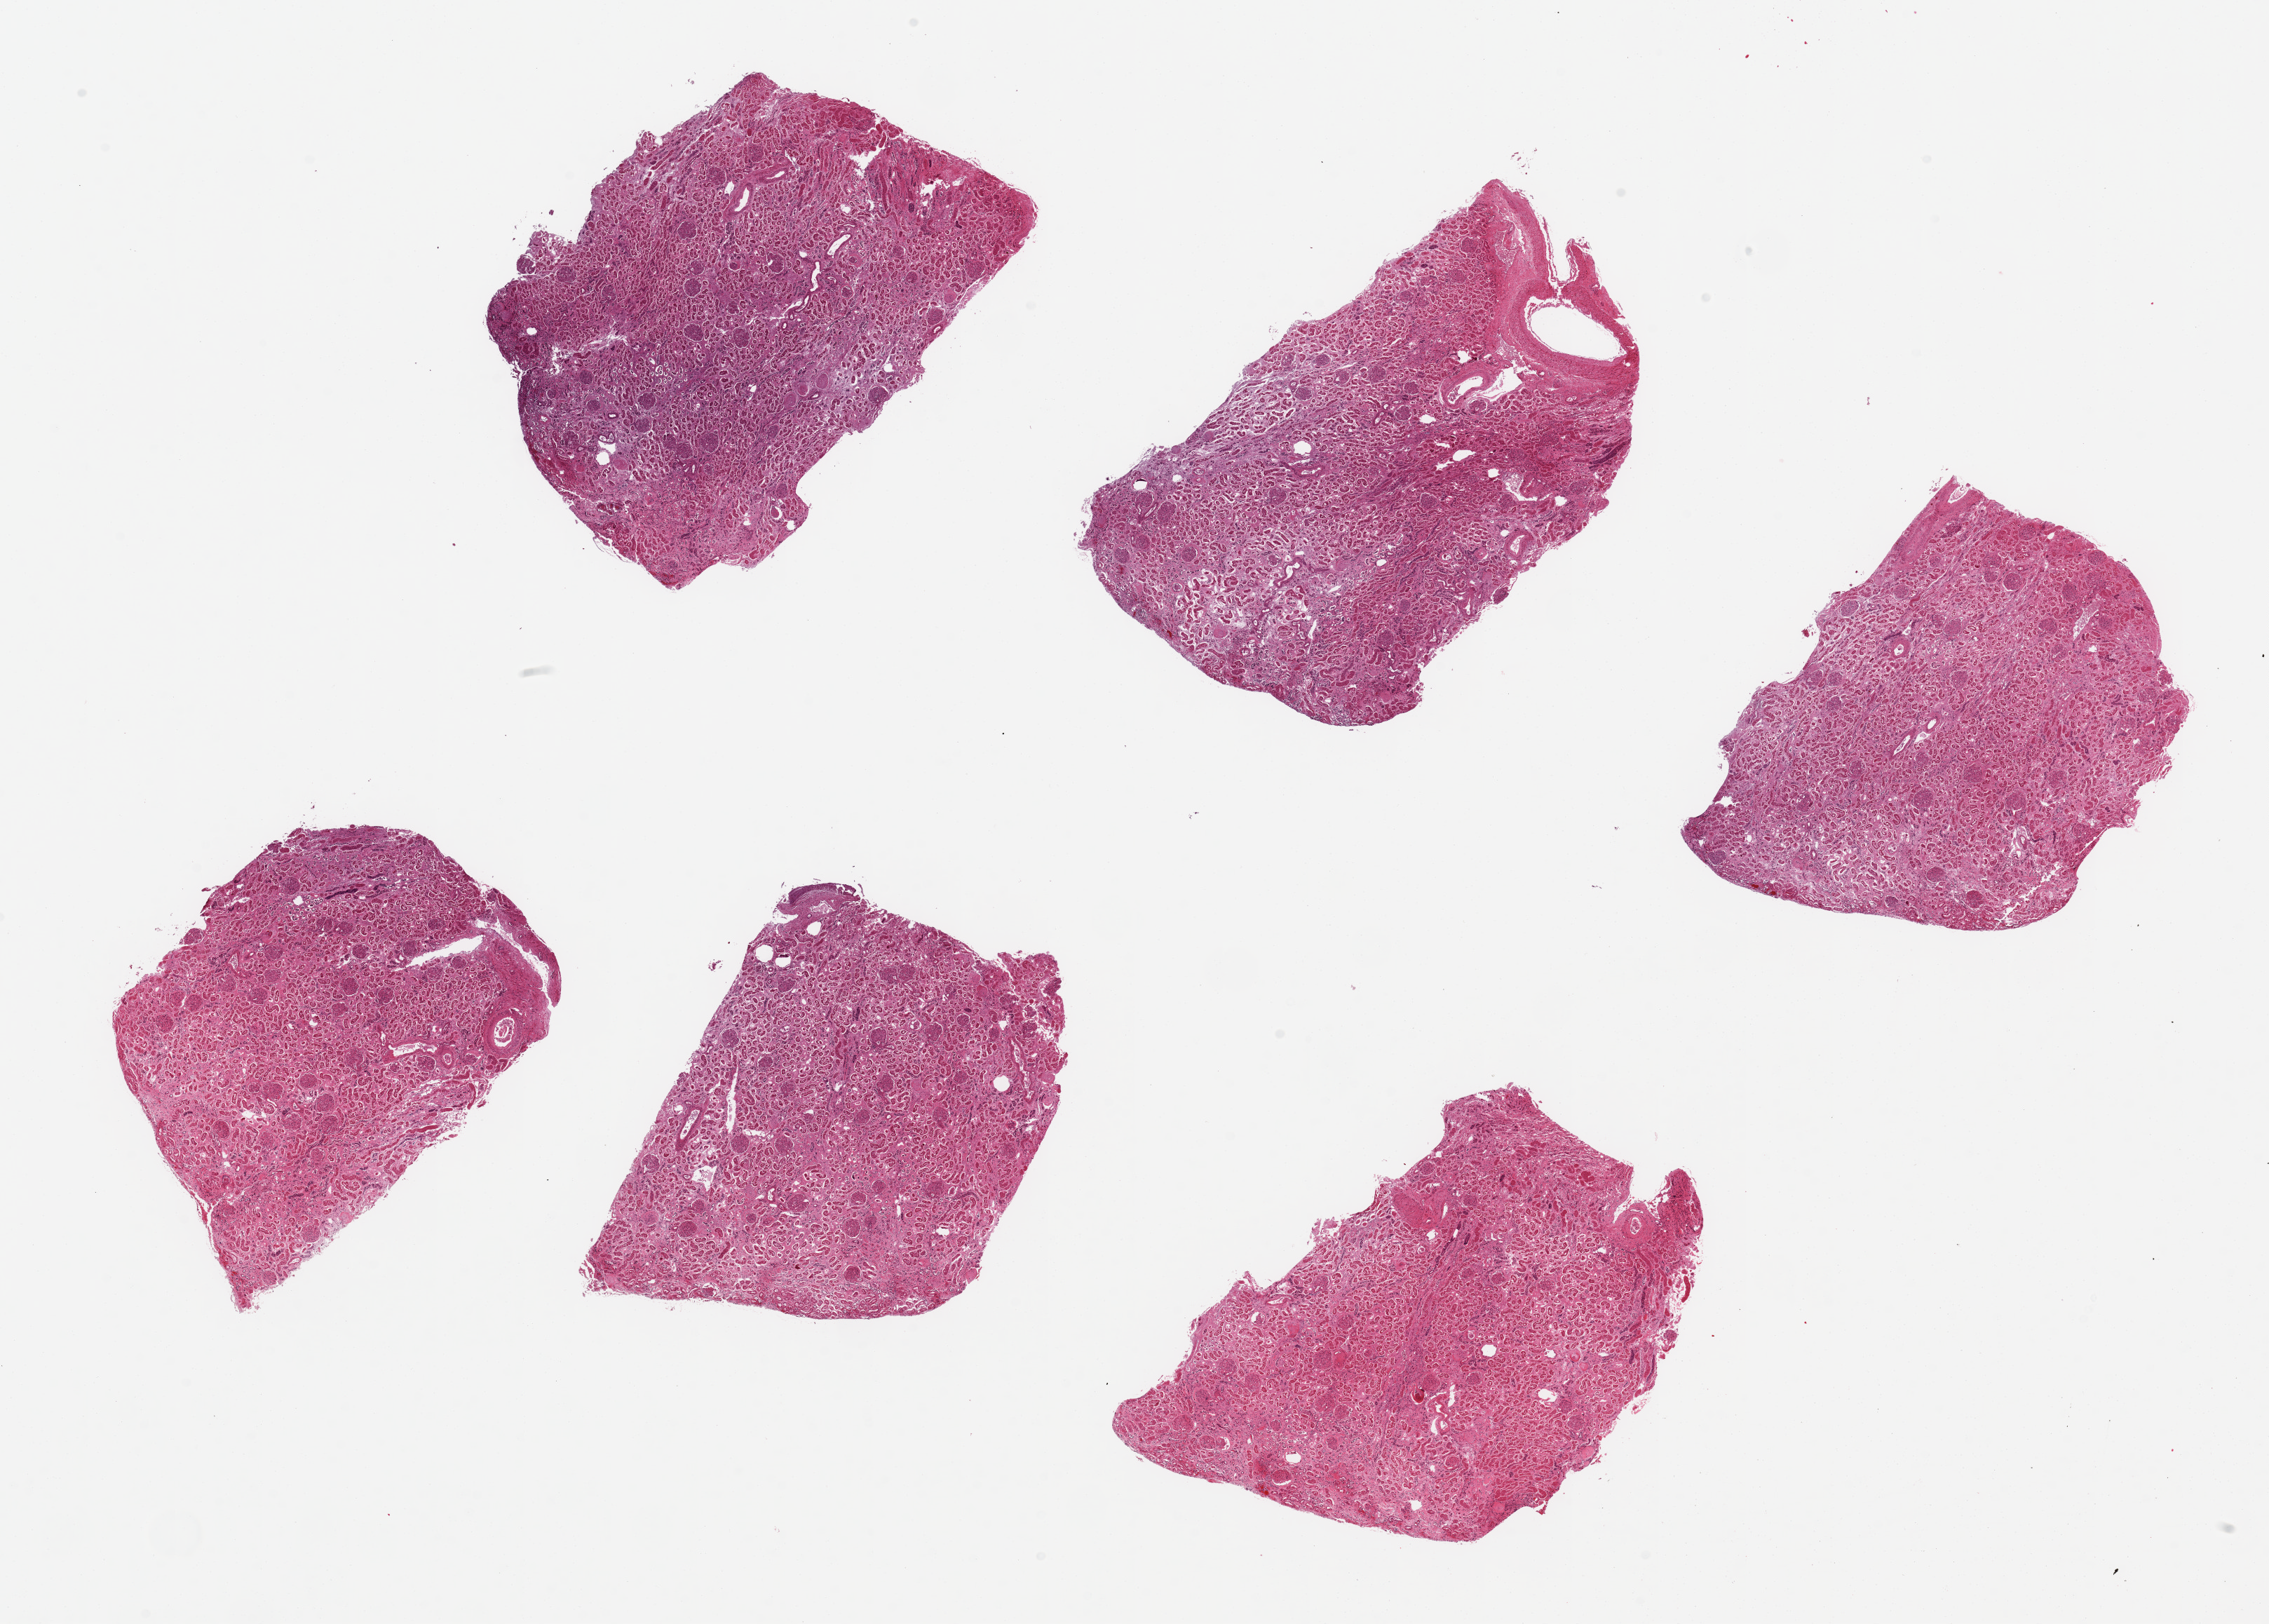
Hematoxylin and eosin (H&E) whole-slide image, a low-resolution overview of the entire scanned area, about 25.6 x 18.3 mm (acquisition: 20x scan). PAXgene-fixed paraffin-embedded (PFPE) section. Sampled site (target tissue): renal cortex. Donor tissue sample.
• pathologist's review note for this sample: 6 pieces up to 6x4 mm; extensive diffuse glomerulosclerosis